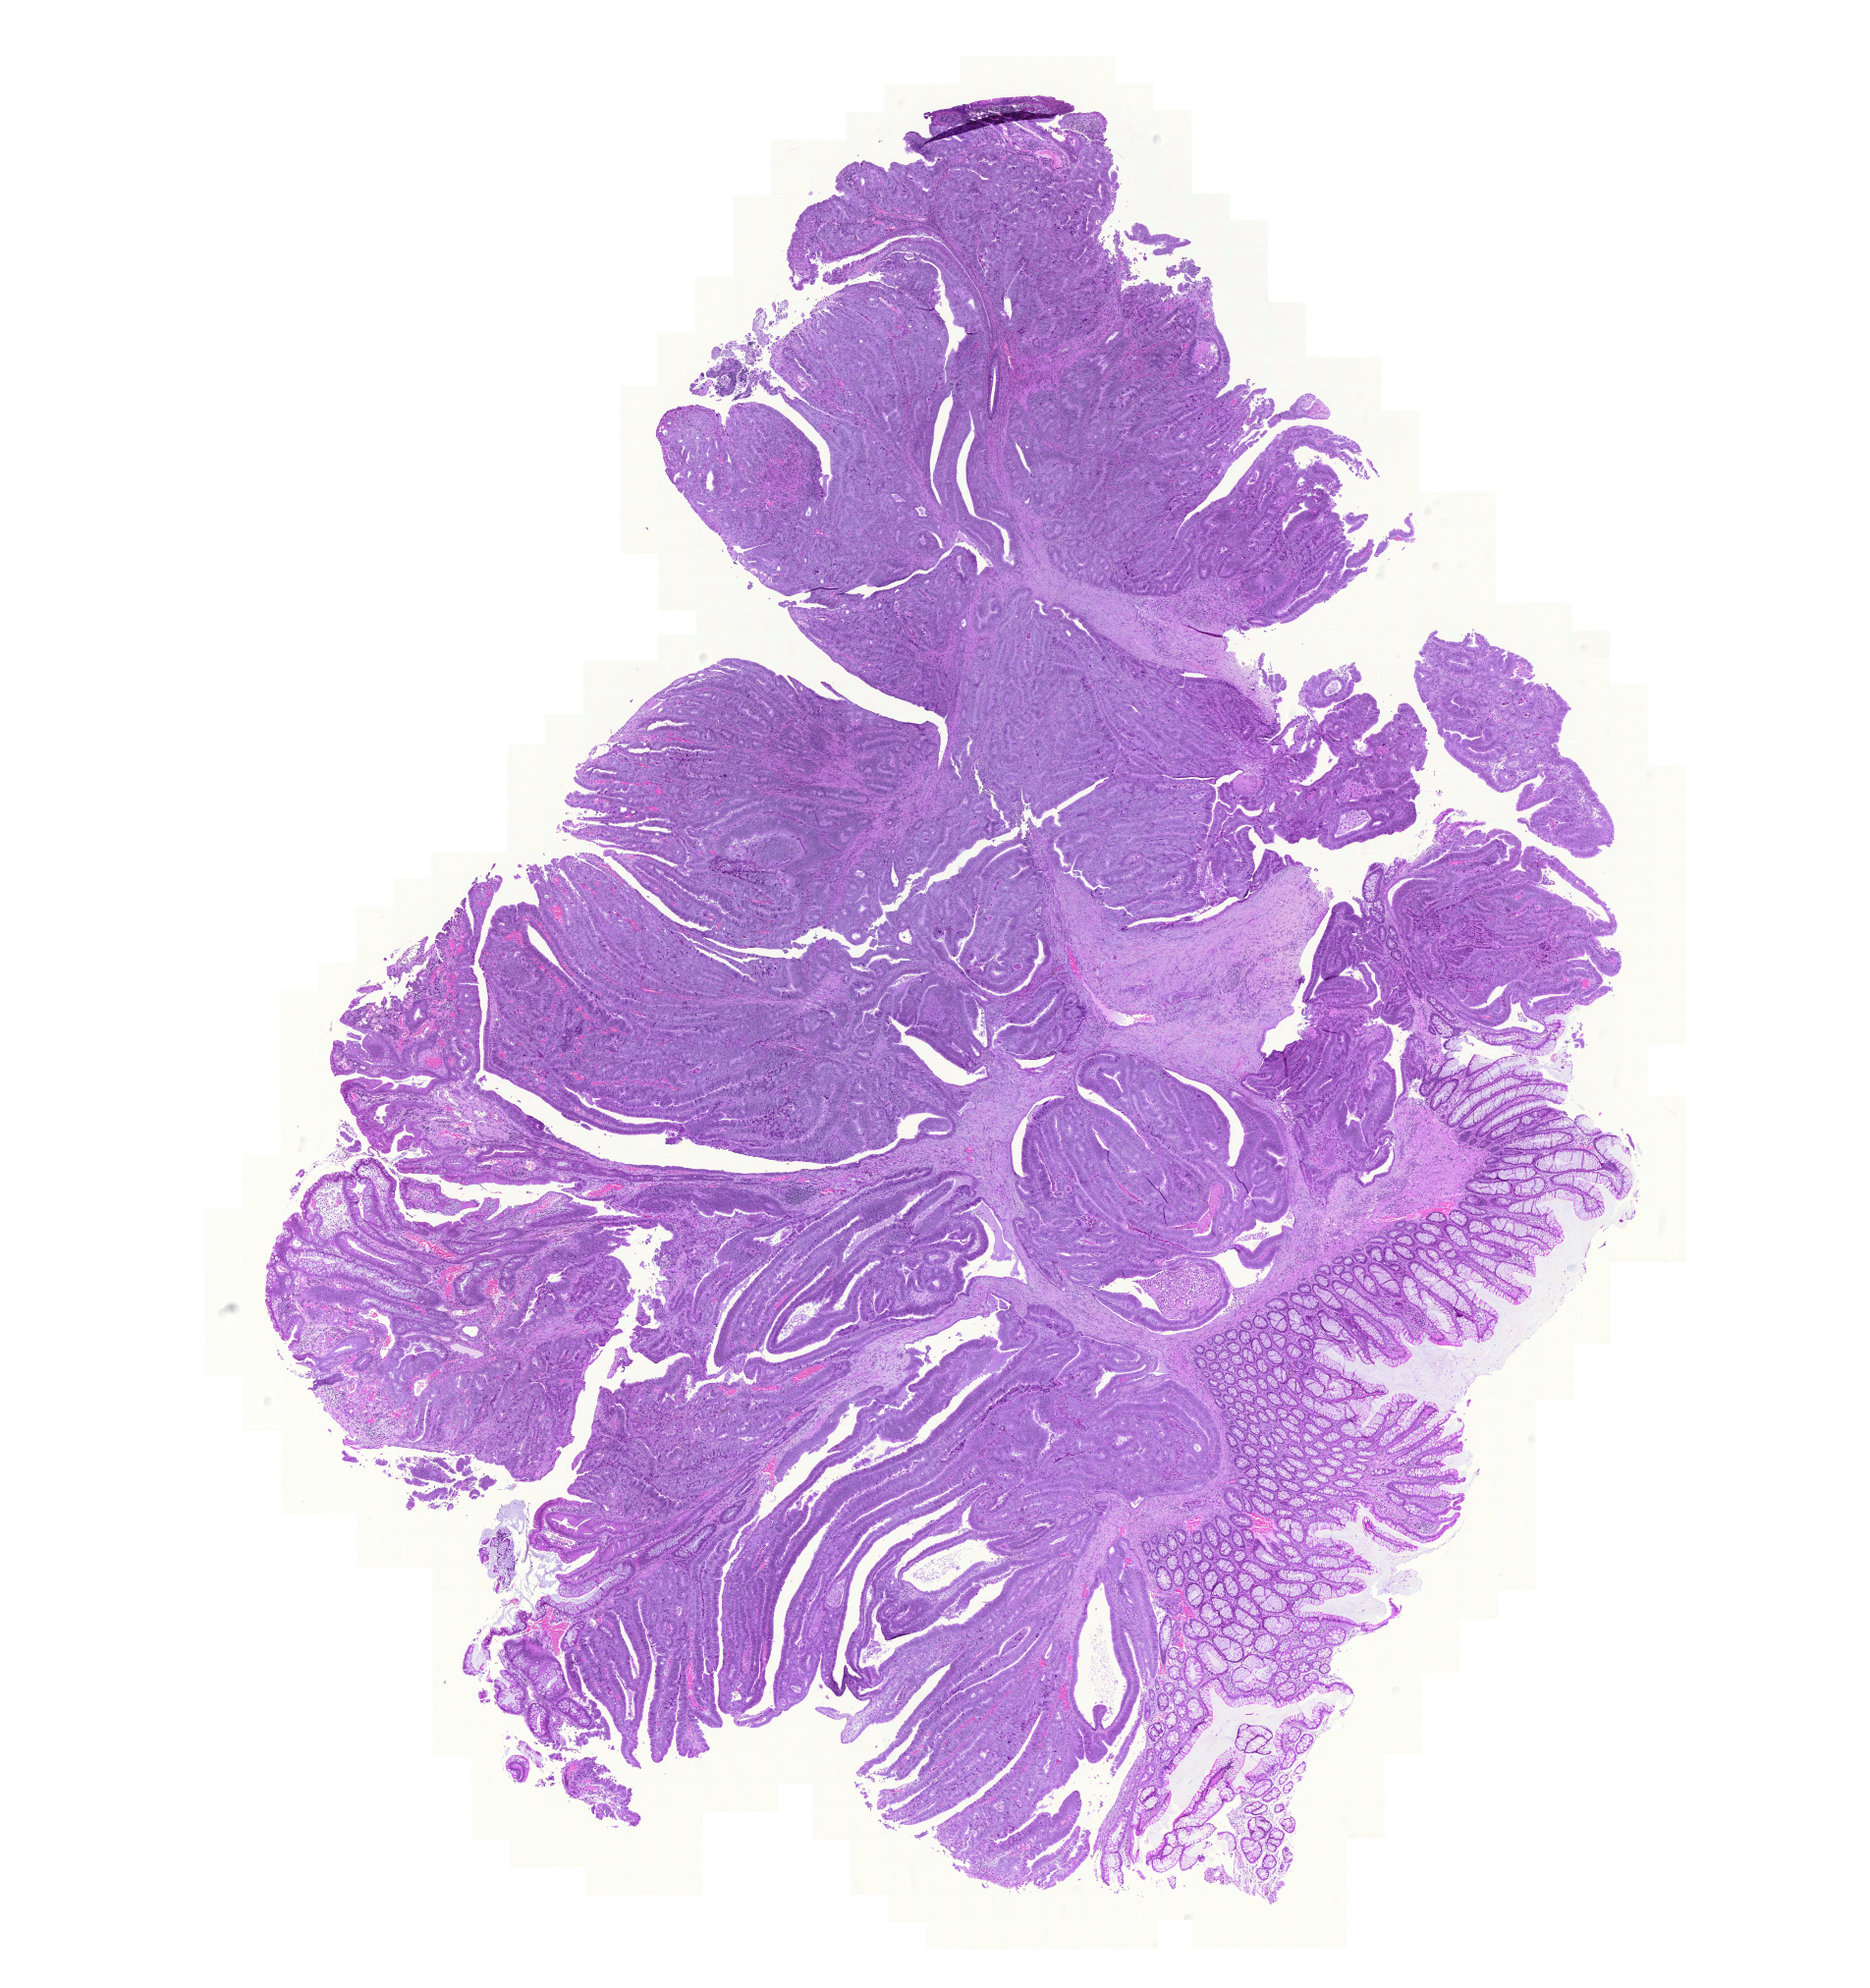
Whole-slide histology image, H&E, a low-resolution overview of the entire scanned area, about 14.2 x 15.1 mm; formalin-fixed paraffin-embedded (FFPE) diagnostic section; primary tumour sample from the colon. Patient: female, age at initial diagnosis 80 years.
AJCC pathologic stage: III. Lymph nodes positive (case pathology): 2 of 14 examined. Diagnosis: Adenocarcinoma, NOS.